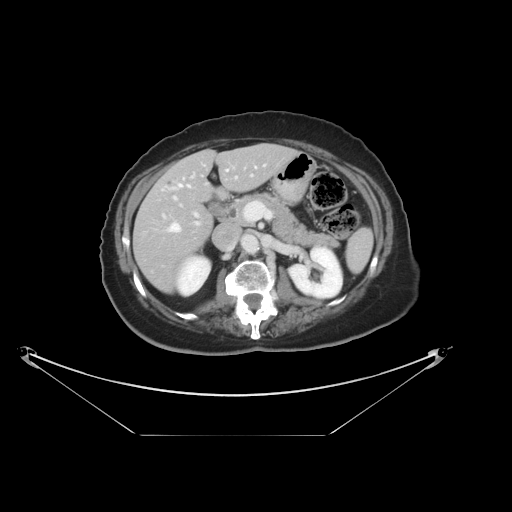
Contrast-enhanced abdominal CT, one axial slice. 120 kVp. Intravenous contrast given. Soft-tissue window (W 400 / L 40 HU). 512 × 512 image matrix, field of view 500 × 500 mm. Female patient, age 70 years. From the clinical record (not read from this slice): diagnosis: colorectal cancer liver metastases, imaged before liver resection; multiple liver metastases: no; largest metastasis: 2.5 cm; chemotherapy before resection: no.
Annotated regions visible in this slice (manually delineated by an expert):
- hepatic veins: bounding box <168,165,265,232> (left, top, right, bottom; pixels)
- liver: <135,145,295,293>
- planned liver remnant (the part of the liver to remain after resection): <135,145,295,292>
- portal vein (with intrahepatic branches): <163,173,253,225>